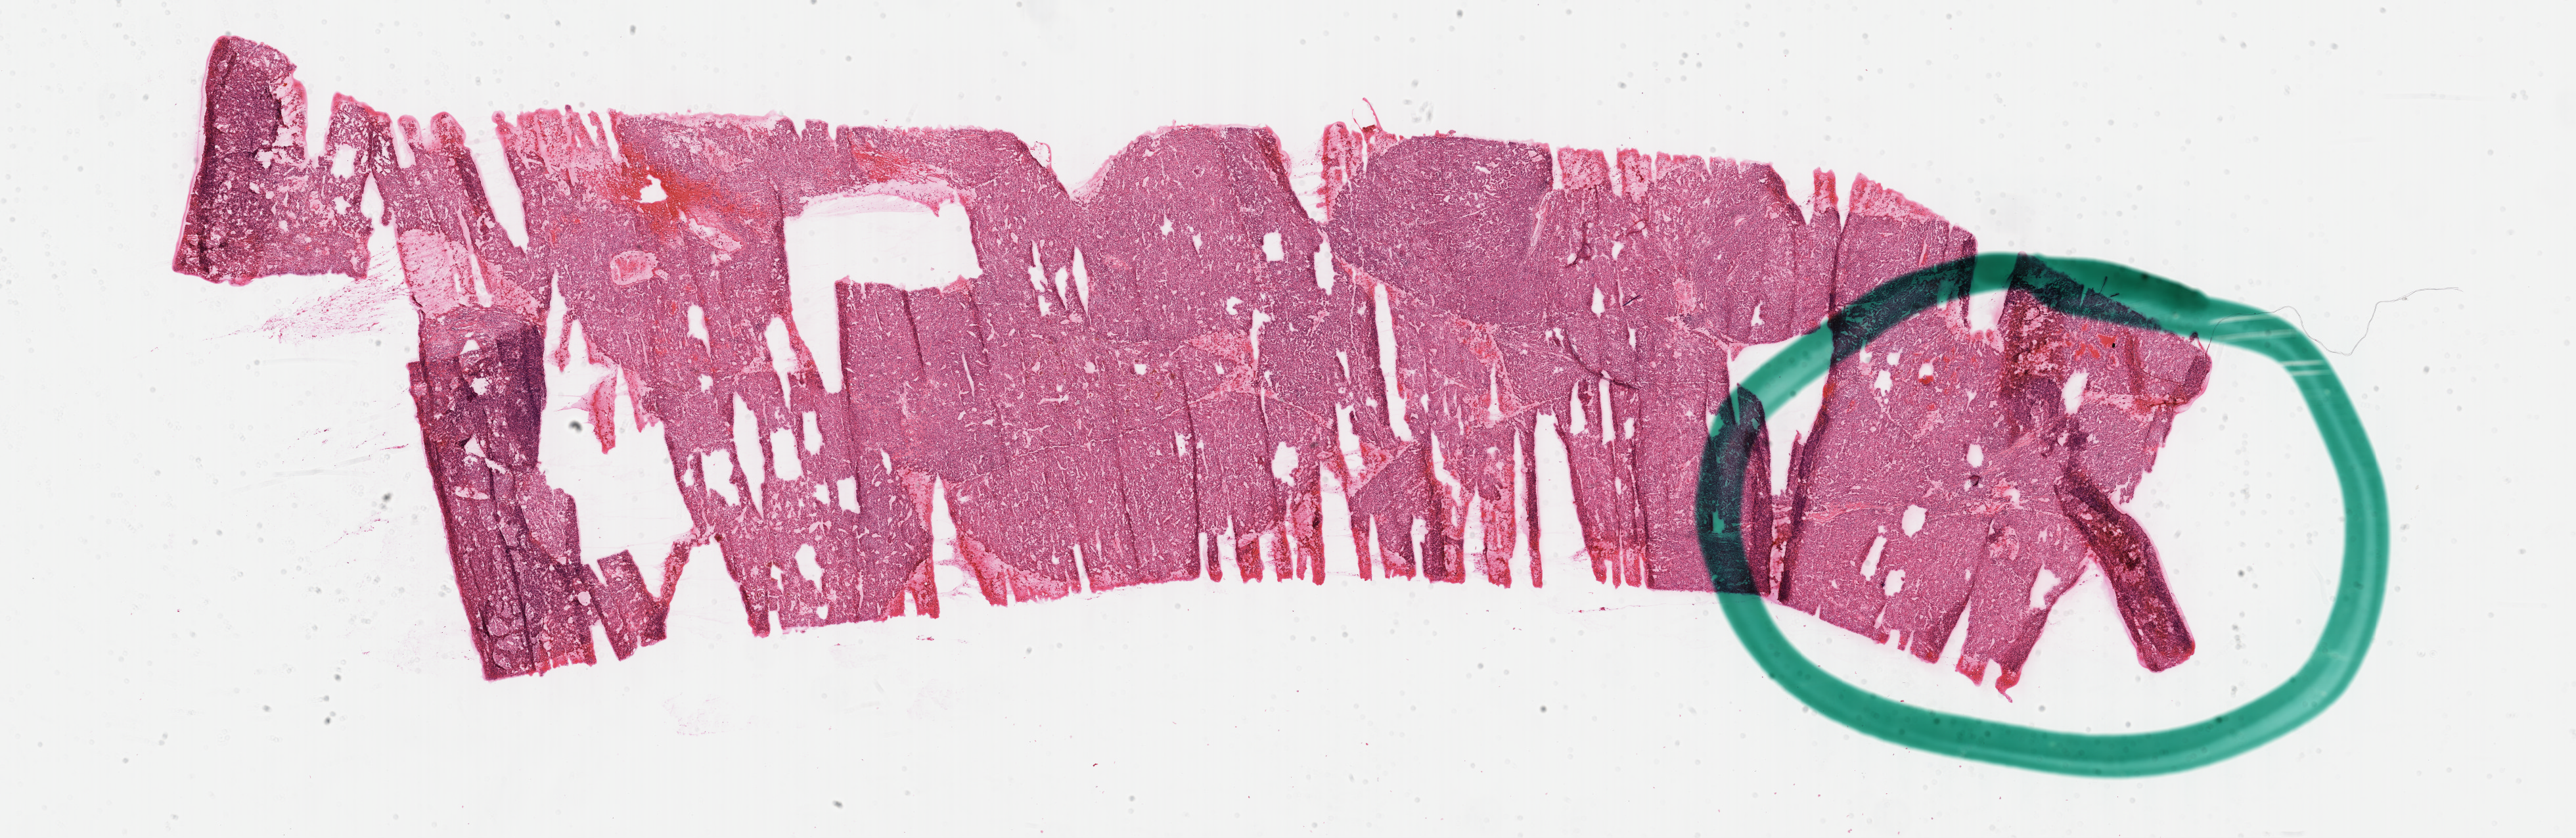
H&E-stained whole-slide image — a low-resolution overview of the entire scanned area, about 31.7 x 10.3 mm, formalin-fixed paraffin-embedded (FFPE) diagnostic section, kidney, primary tumour sample. Patient: male, age at initial diagnosis 70 years. Histologic grade: G3 (poorly differentiated).
AJCC pathologic stage: II. Diagnosis: Clear cell adenocarcinoma, NOS.